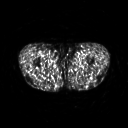
FDG PET of an extremity soft-tissue mass (from a PET/CT study), one axial slice; slice 262 of 311 in the series (ordered by position); 3.27 mm slice thickness; 128 × 128 image matrix, field of view 500 × 500 mm. Patient: male, 29 years. From the clinical record (not read from this slice): histological type: mixoid liposarcoma; grade: low; site of the primary tumour: left thigh.
Outlined on this slice (expert contour drawn on MRI and transferred to this co-registered scan by the dataset authors):
- gross tumour volume (mass): box from (x=75, y=58) to (x=81, y=64) px